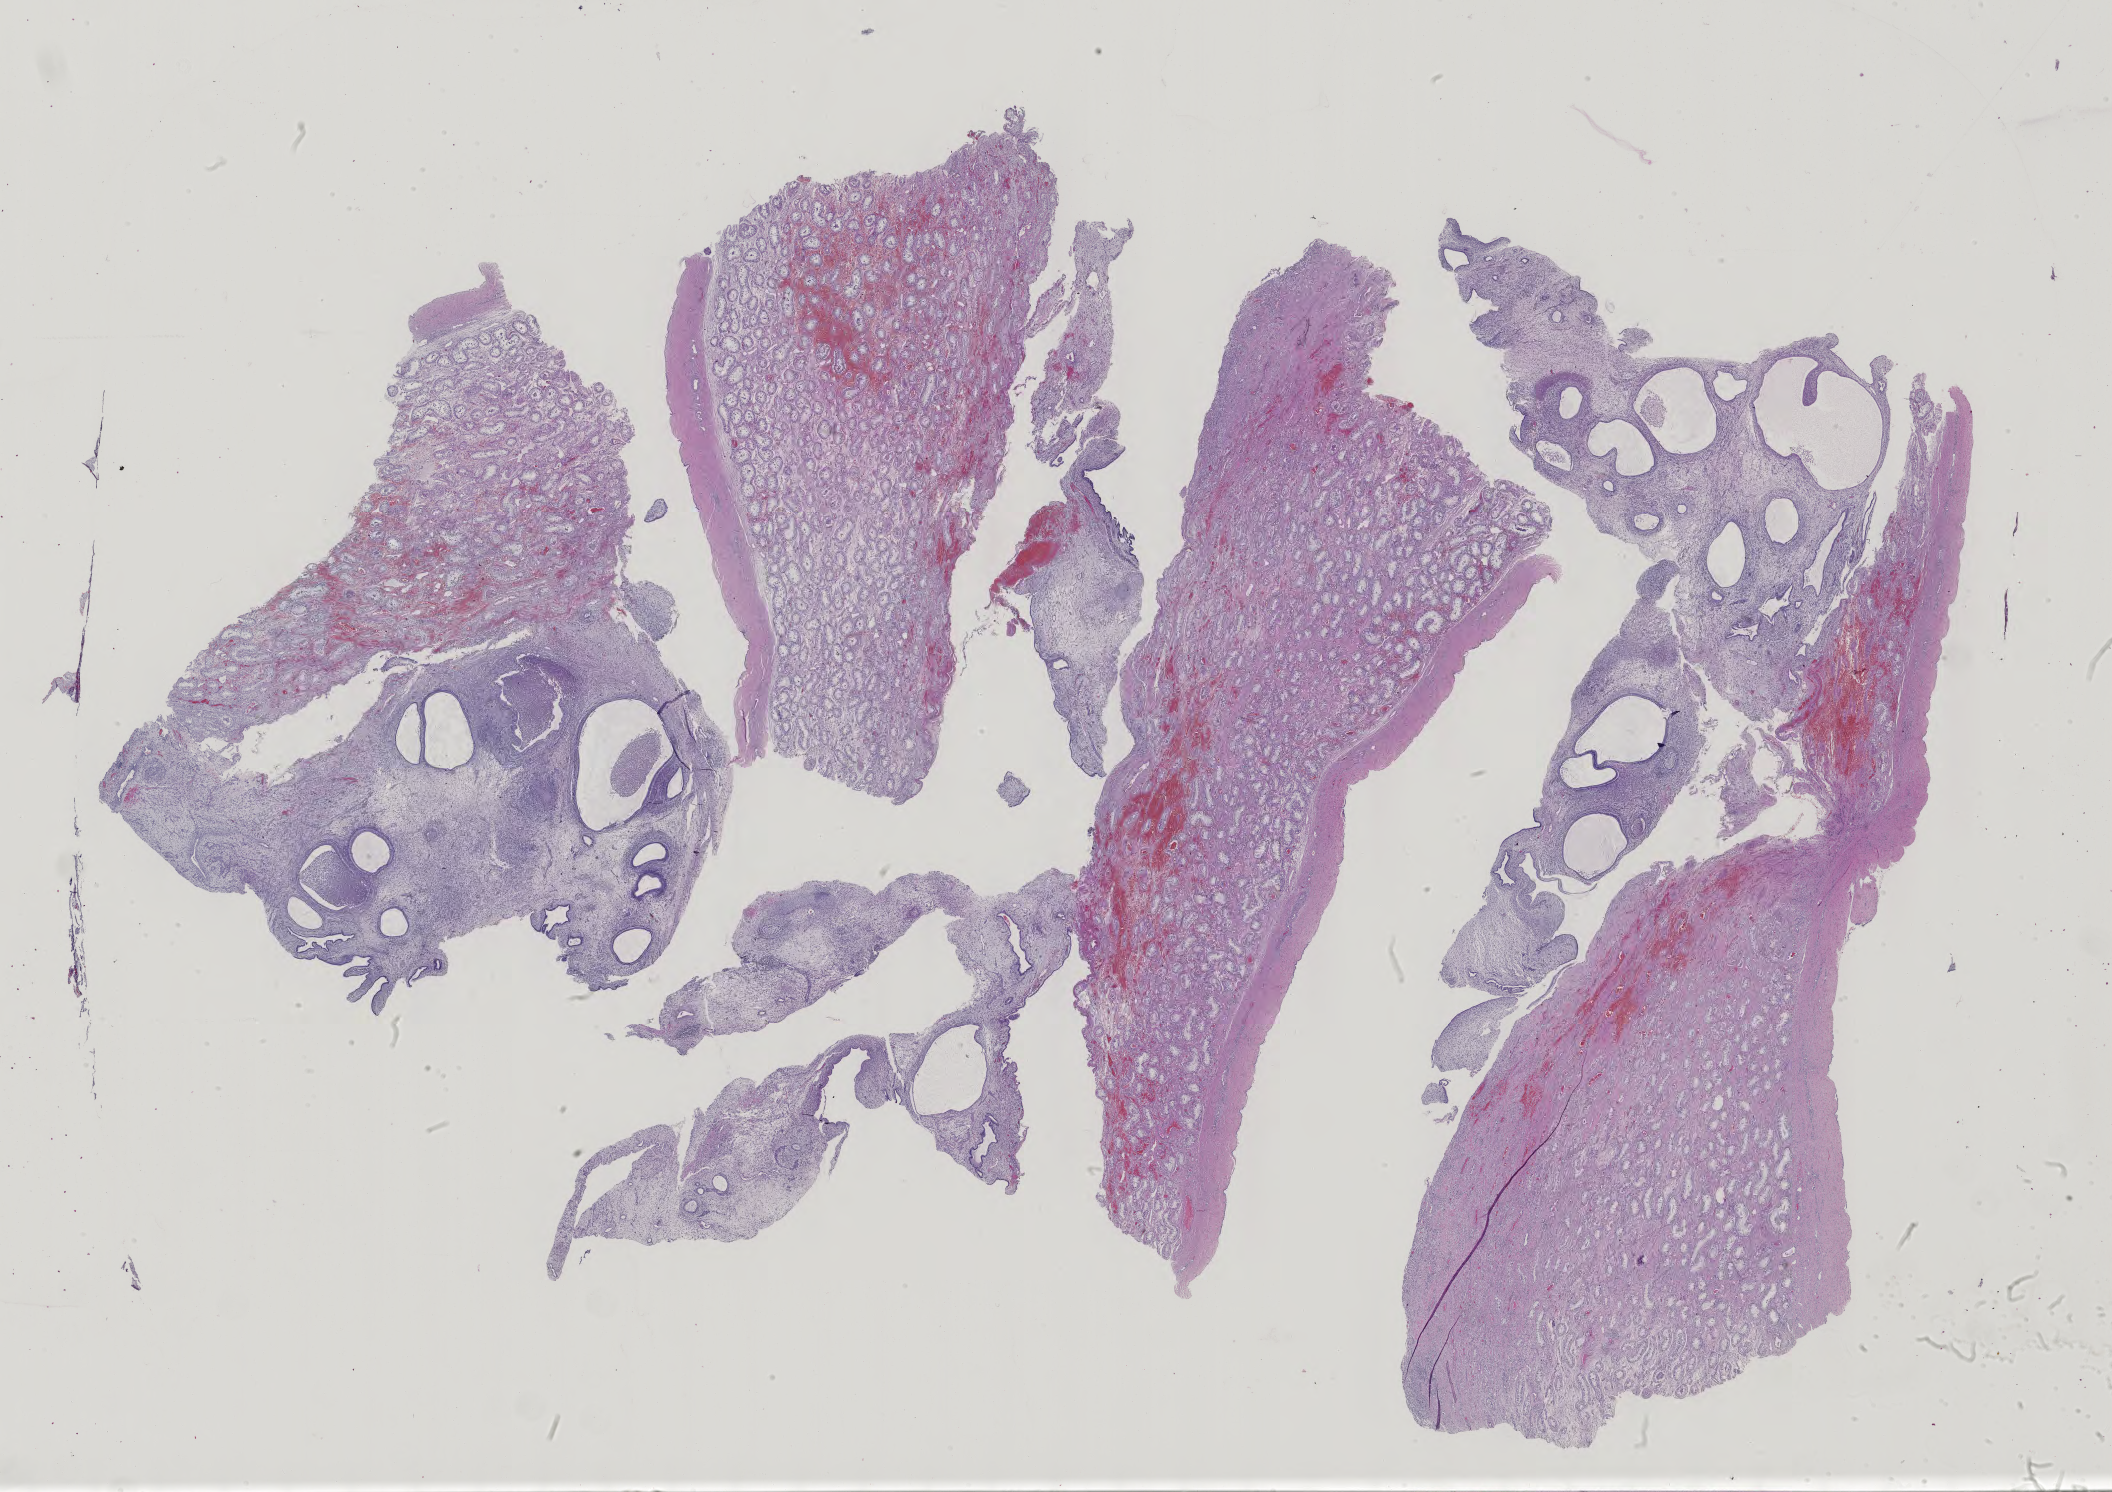
Hematoxylin and eosin (H&E) stained whole-slide image, low-resolution overview of the scanned area, about 30.8 x 21.7 mm. Patient sex: male.
Specimen: FFPE section; primary tumour sample from the testis.